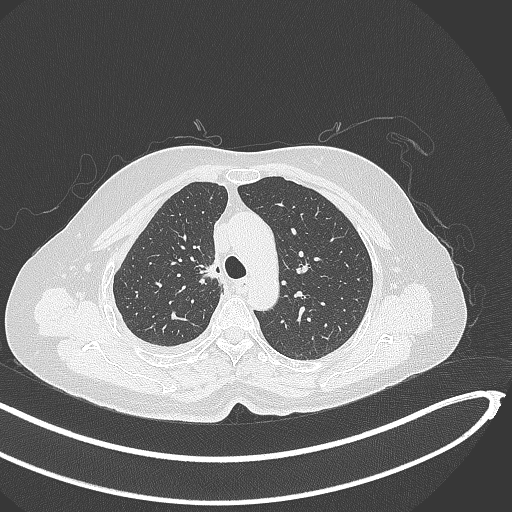
Chest CT, one axial slice; slice 274 of 345 in the series (ordered by position); reconstruction kernel B70f; 120 kVp; lung window (W 1500 / L -600 HU); 1 mm slice thickness; 512 × 512 image matrix, field of view 400 × 400 mm. Female patient, age 64 years. From the clinical record (not read from this slice): clinical TNM (as recorded): T1b N0 M1.
Outlined on this slice (bounding box drawn by a radiologist):
- lung tumour (recorded histology: adenocarcinoma): bounding box [x1, y1, x2, y2] px = [199, 252, 223, 286]